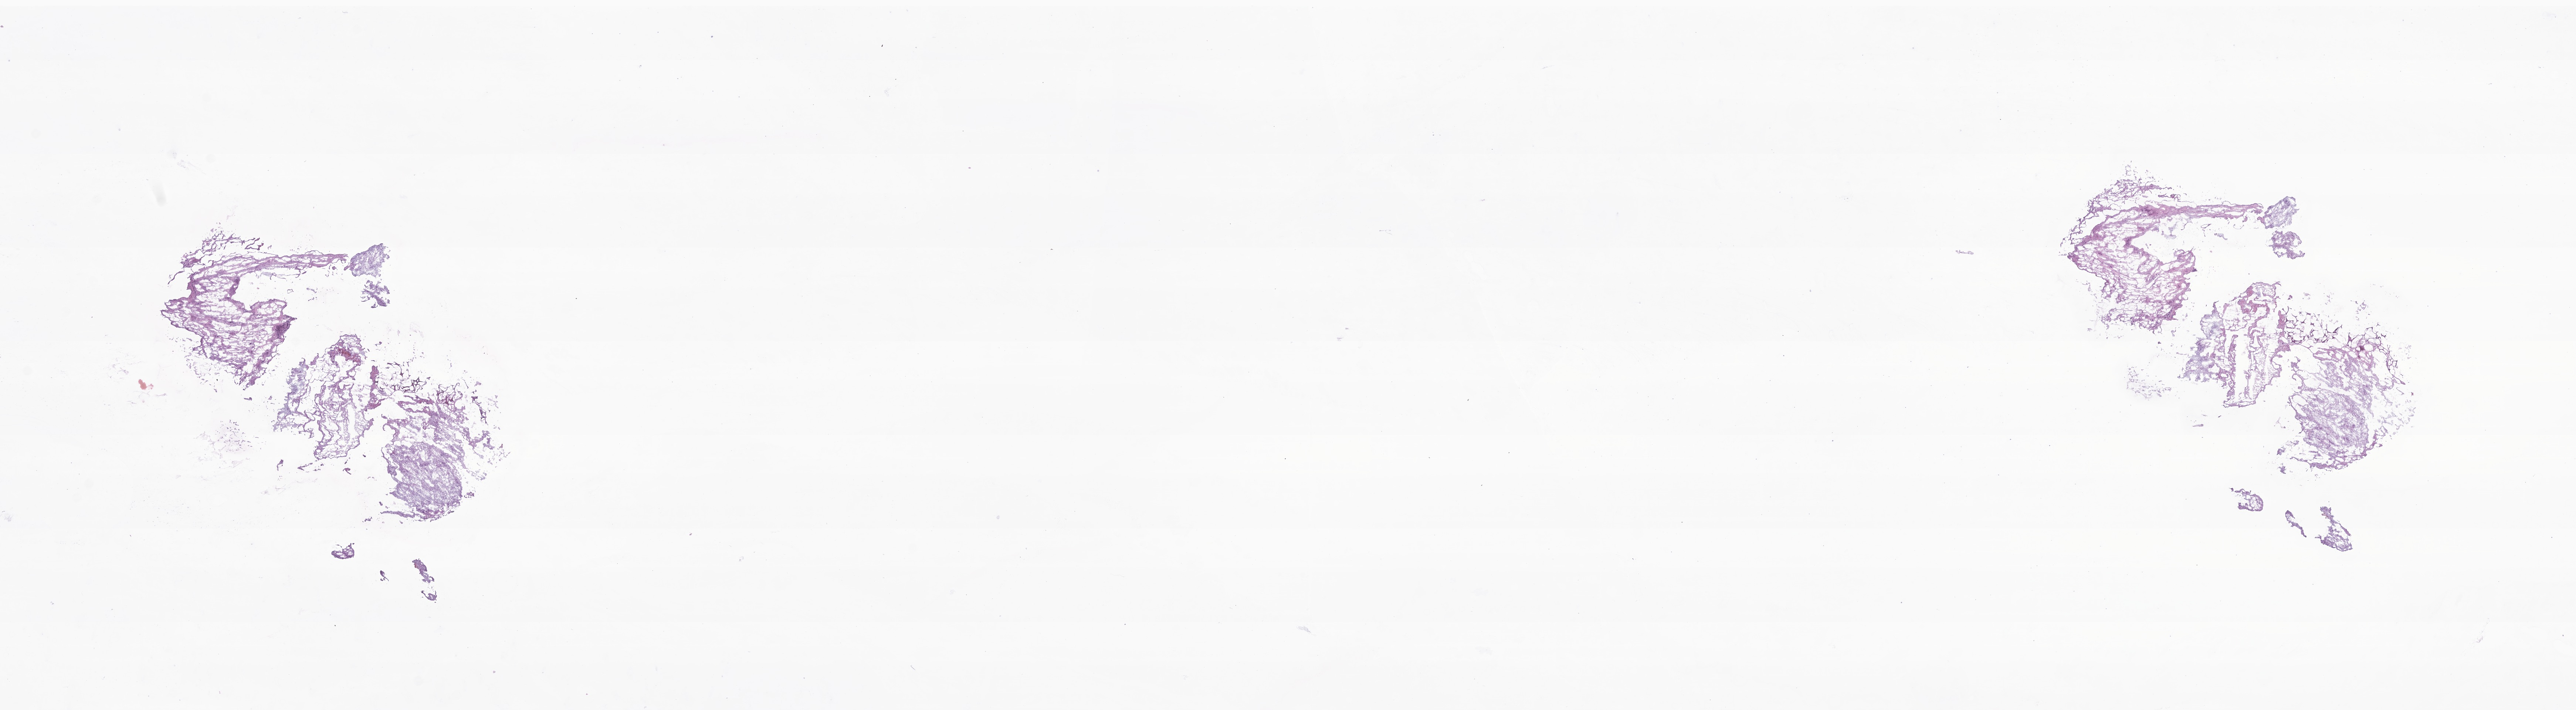
Hematoxylin and eosin (H&E) whole-slide image of tumor tissue from the spinal cord — shown as a low-resolution overview of the whole scanned area (about 29.4 x 8.1 mm), frozen section. Male patient, age 168 months.
* recorded diagnosis: Neuroma, NOS